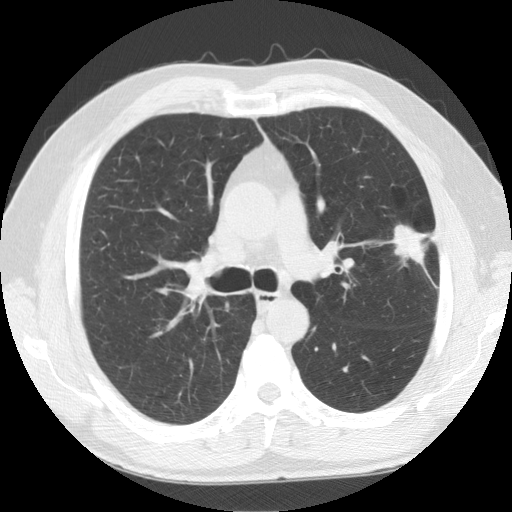
Axial slice from a low-dose chest CT screening exam; baseline screening round; lung window (W 1500 / L -600 HU); 2.5 mm slice thickness; standard (soft-tissue) reconstruction kernel (STANDARD); 120 kVp. Male, age 59 years at enrolment. Former smoker at enrolment.
• Lesion marked by an expert reader, bounding box [x1, y1, x2, y2] px = [374, 204, 455, 283].
• Reader record for this screening exam (exam-level; its link to the box is not recorded): non-calcified nodule or mass ≥4 mm, left upper lobe, 23 × 23 mm, spiculated (stellate) margins, soft tissue attenuation.
• Later outcome: lung cancer diagnosed 28 days after this screen — squamous cell carcinoma, NOS, left upper lobe, moderately differentiated (G2), stage IA (AJCC 6th edition), 27 mm at pathology.